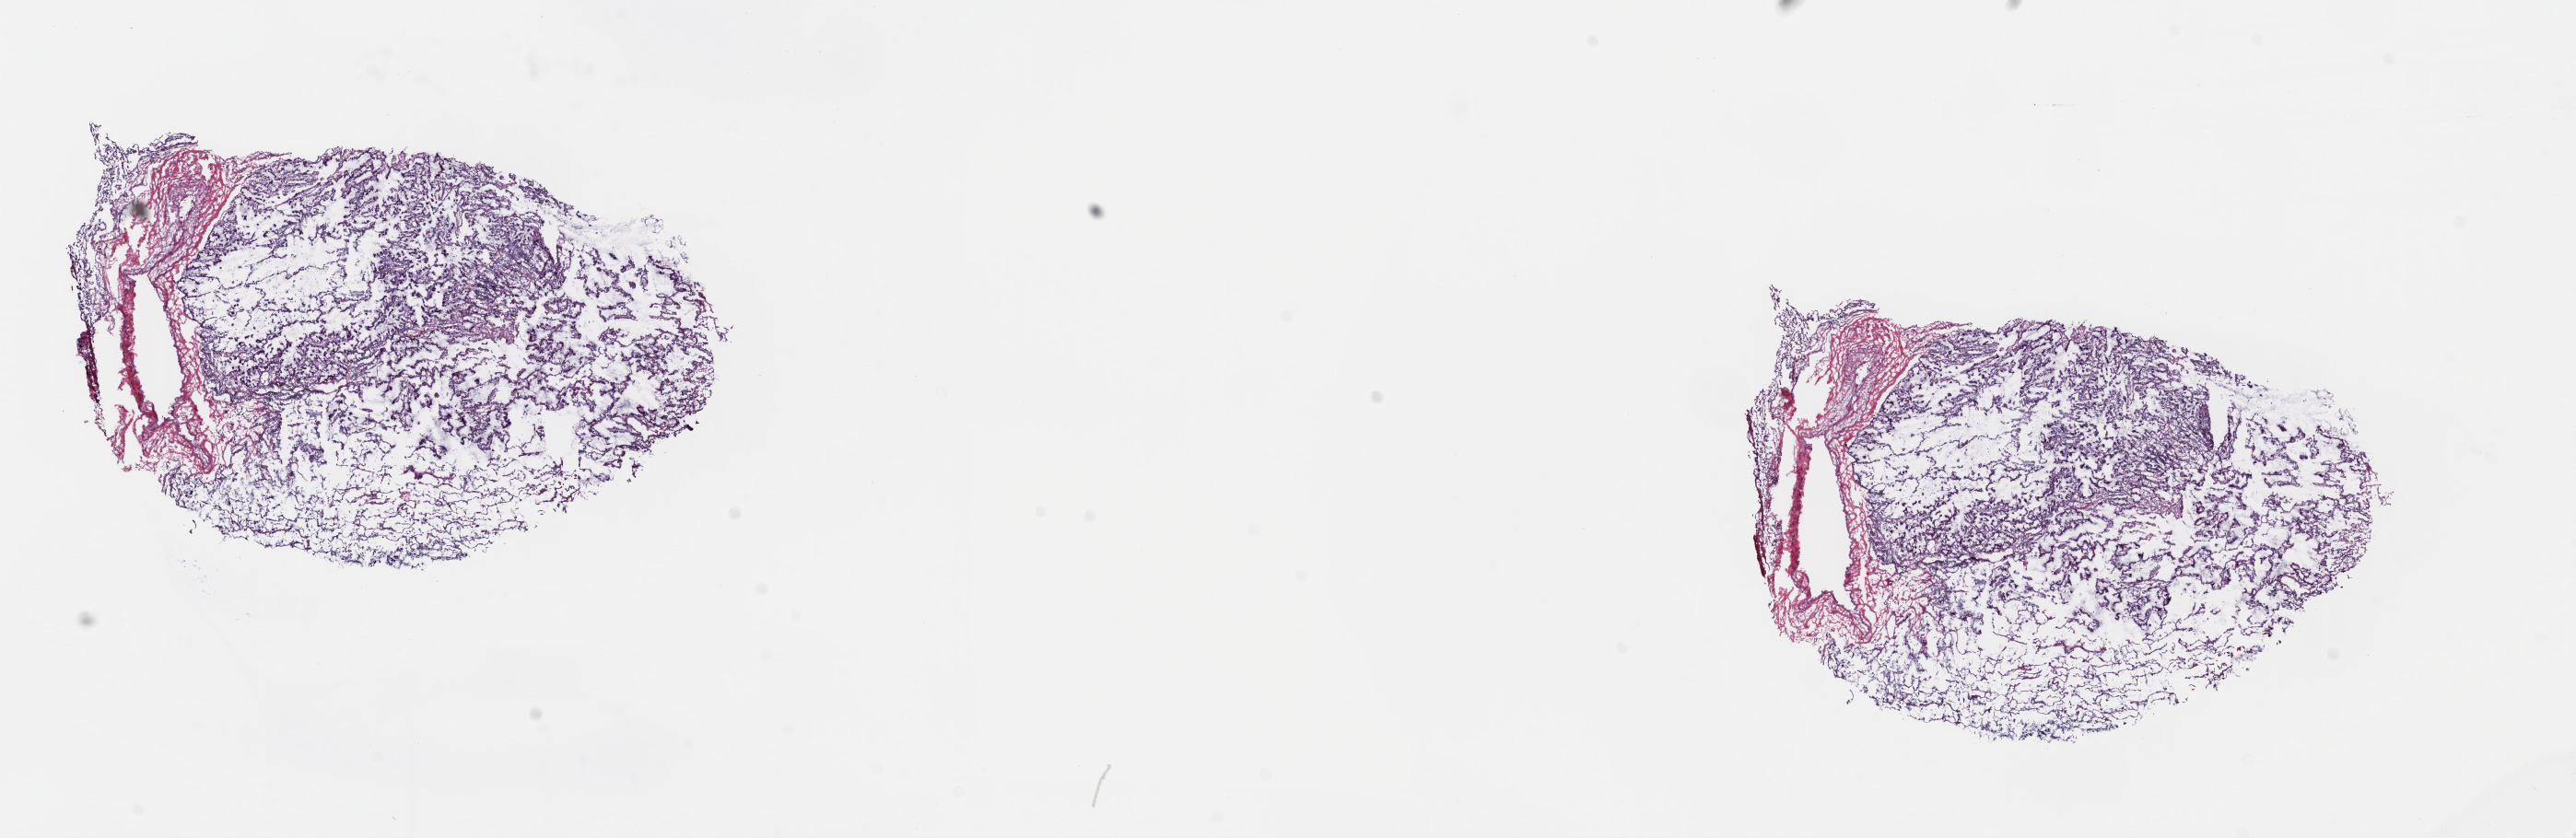
Whole-slide histology image, H&E — a low-resolution overview of the entire scanned area, about 22.0 x 7.2 mm (acquisition: 40x scan); frozen section; lung, primary tumour sample. Female patient; age at initial diagnosis 56 years. Composition of this section per pathologist review: tumour cells 85%, tumour nuclei 100%, normal cells 0%, stromal cells 15%, necrosis 0%. Infiltration values recorded for this section: lymphocyte infiltration 0%, monocyte infiltration 2%, neutrophil infiltration 0%.
TNM: T1b N1 M0. AJCC pathologic stage: IIA (7th edition). Histologic diagnosis: Mucinous adenocarcinoma (upper lobe, lung).